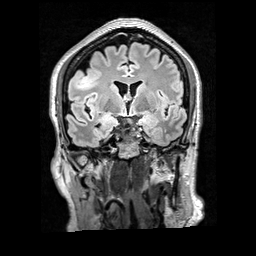
Brain MRI from a brain-tumour surgery series, one coronal slice. Slice 111 of 200 in the series (ordered by position). T2 FLAIR. 1 mm slice thickness. 256 × 256 image matrix. From the clinical record (not read from this slice): histopathology: Glioblastoma; WHO grade: 4; IDH mutation: no.
Outlined on this slice (expert manual segmentation):
- tumour: bounding box (x1, y1, x2, y2) in pixels: (74, 71, 102, 91)